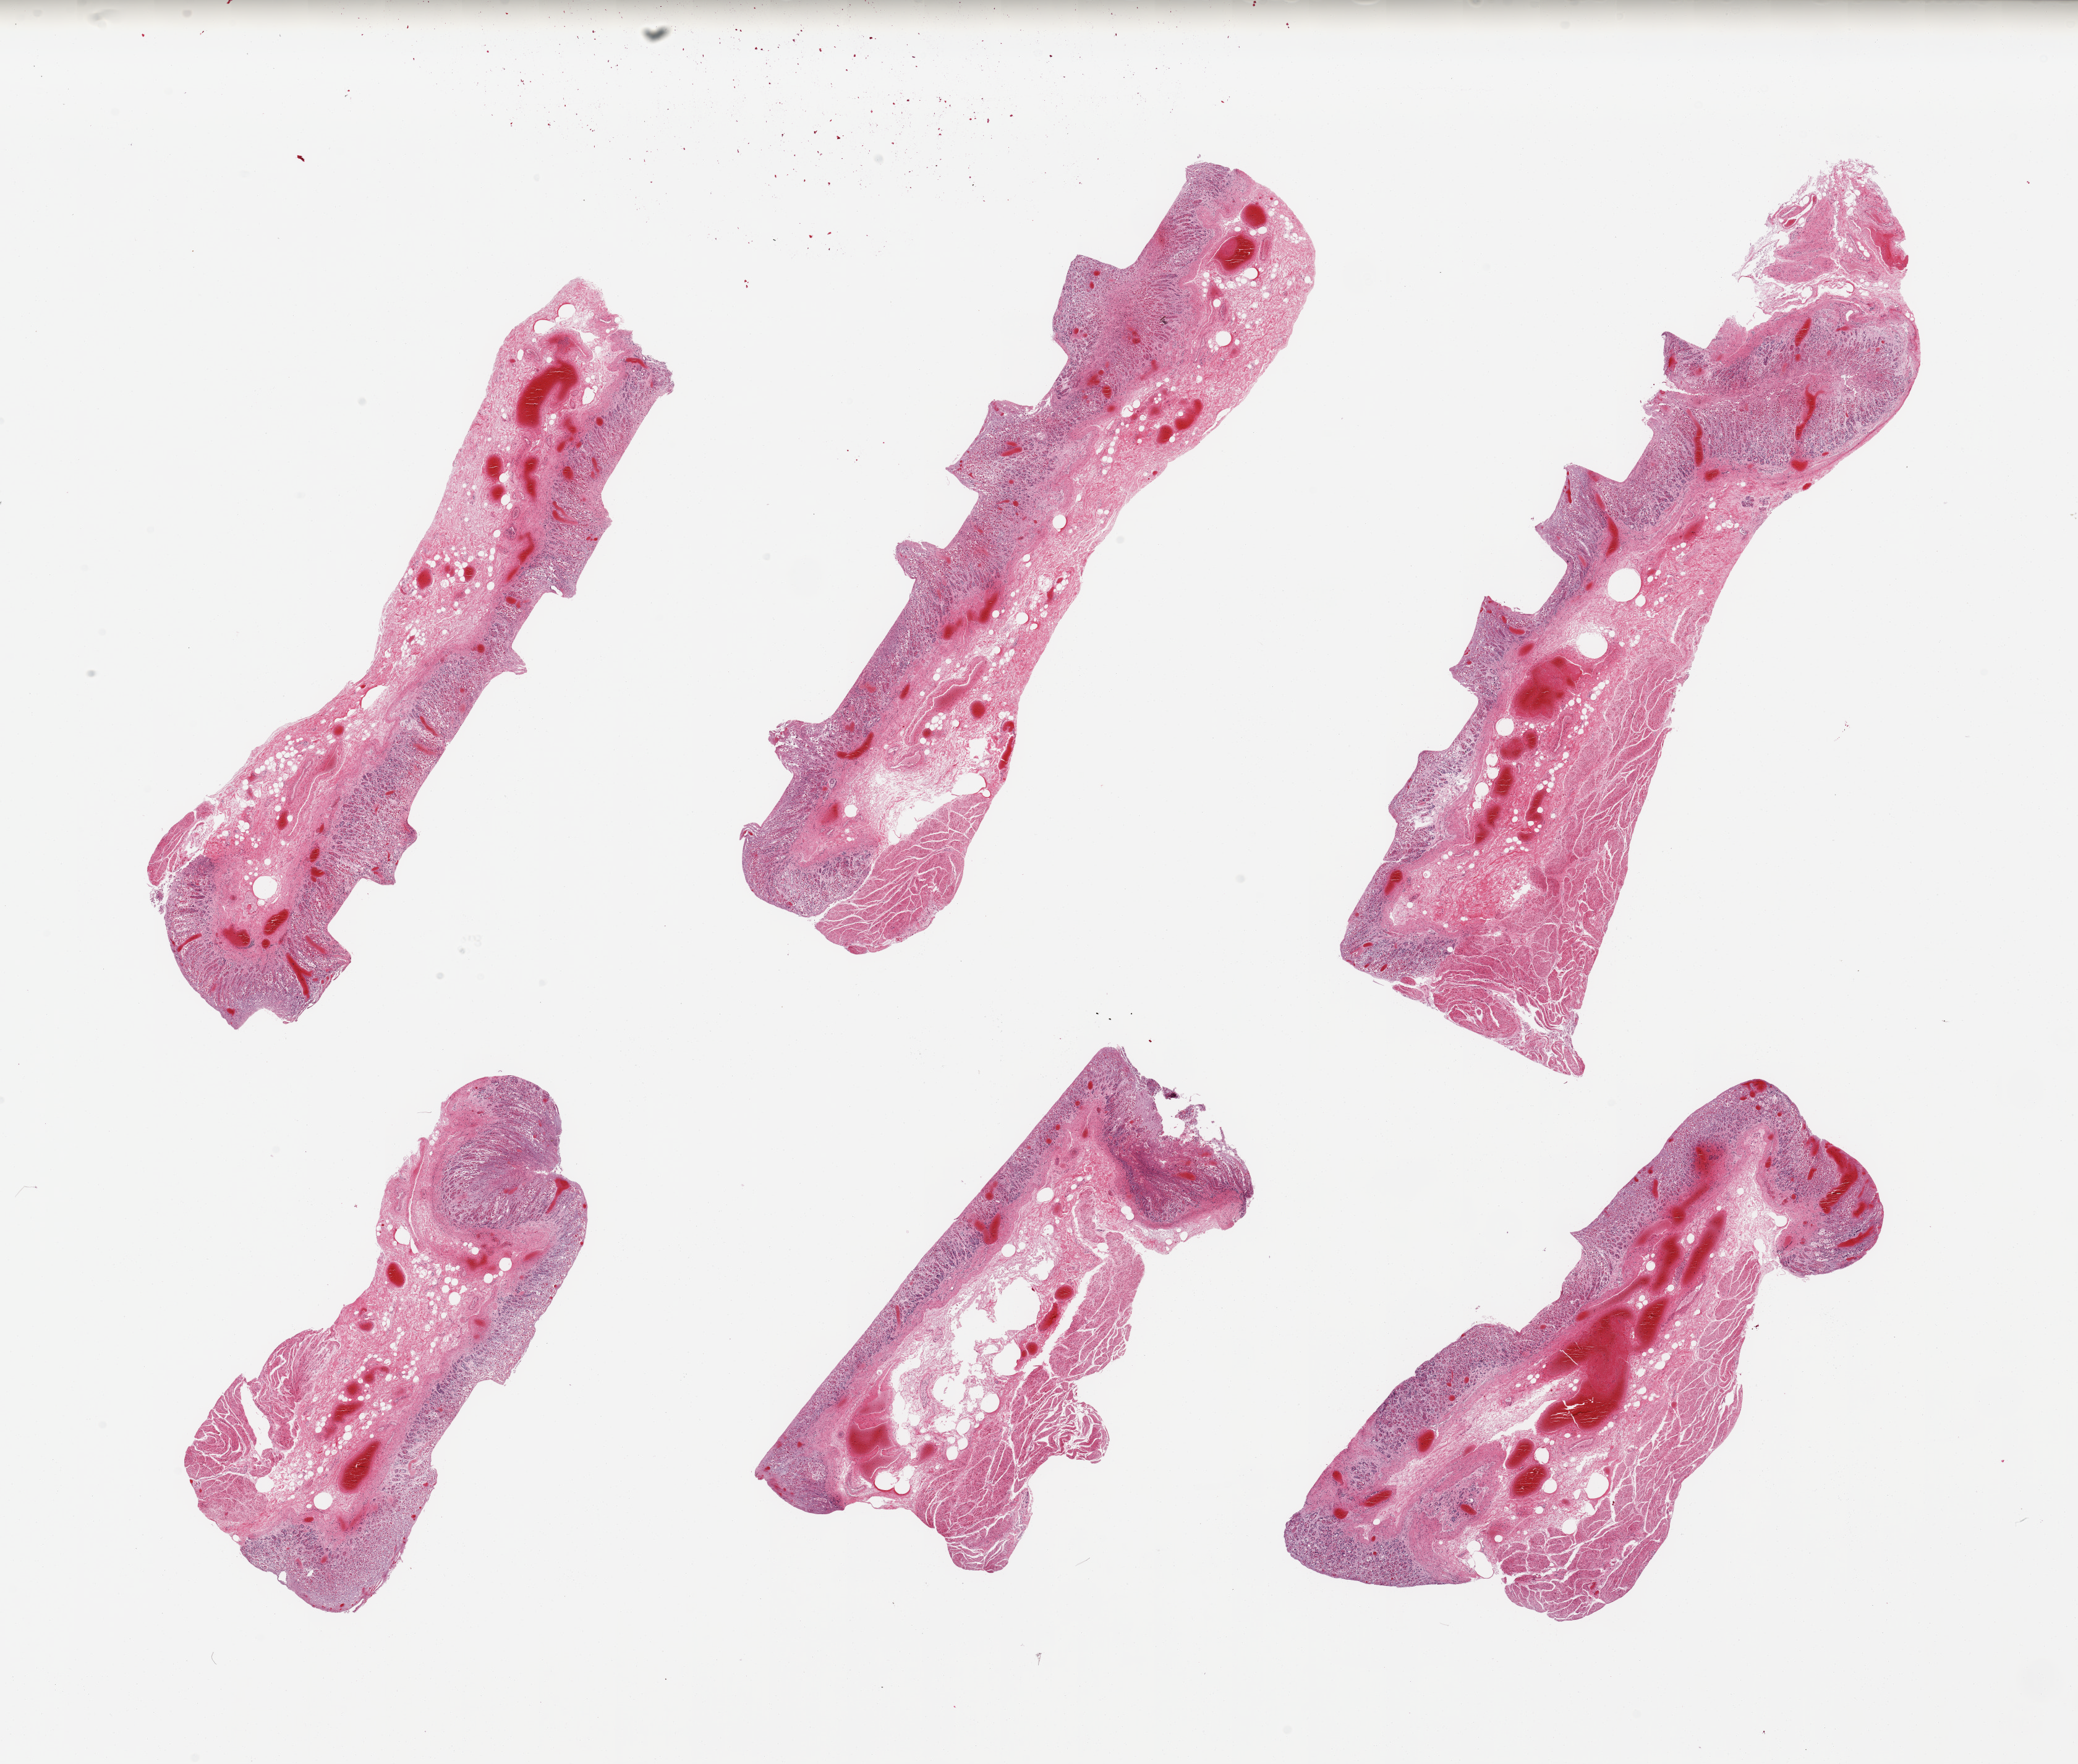
Hematoxylin and eosin (H&E) whole-slide image, brightfield — low-resolution overview of the scanned area, about 26.6 x 22.6 mm; PAXgene-fixed, paraffin-embedded tissue; target tissue: stomach; tissue donor sample. Donor sex: male.
Reviewer comment on this tissue sample: 6 pieces; severely autolyzed mucosa; limited amount of muscularis.